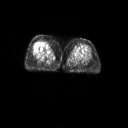
FDG PET of an extremity soft-tissue mass (from a PET/CT study), one axial slice; position 14 of 267 along the scan axis; 128 × 128 image matrix. Female patient, age 56 years. From the clinical record (not read from this slice): histological type: malignant solitary fibrous tumor; grade: intermediate; site of the primary tumour: right thigh.
Structures marked on this image (expert contour drawn on MRI and transferred to this co-registered scan by the dataset authors):
- gross tumour volume including surrounding oedema: box from (x=41, y=41) to (x=51, y=48) px